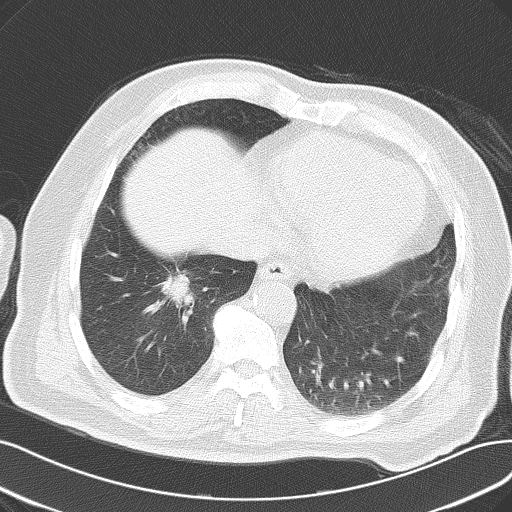
Chest CT, one axial slice. Position 24 of 61 along the scan axis. Reconstruction kernel B70f. 120 kVp. Lung window (W 1500 / L -600 HU). 5 mm slice thickness. 512 × 512 image matrix, field of view 363 × 363 mm. Male patient, age 69 years. Case-level facts recorded for this patient, not image findings: clinical TNM (as recorded): T1c N0 M0; histopathological grade: G2-3.
Outlined on this slice (rectangle marked by the reading radiologist):
- lung tumour (recorded histology: adenocarcinoma): bounding box [x1, y1, x2, y2] px = [160, 268, 188, 317]